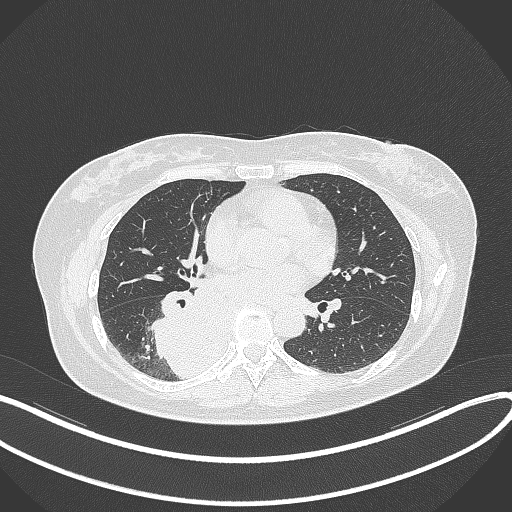
Chest CT, one axial slice. Slice 170 of 331 in the series (ordered by position). Reconstruction kernel B70f. Lung window (W 1500 / L -600 HU). 1 mm slice thickness. 512 × 512 image matrix. Patient: female, 54 years. From the clinical record (not read from this slice): clinical TNM (as recorded): T4 N0 M0.
Structures marked on this image (bounding box drawn by a radiologist):
- lung tumour (recorded histology: adenocarcinoma): bounding box <148,289,226,379> (left, top, right, bottom; pixels)